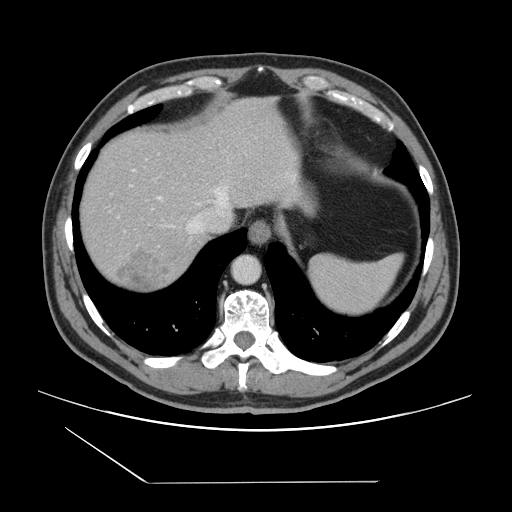
Contrast-enhanced abdominal CT, one axial slice. Position 124 of 157 along the scan axis. 120 kVp. Intravenous contrast given. Soft-tissue window (W 400 / L 40 HU). 512 × 512 image matrix, field of view 407 × 407 mm. Male patient, age 61 years. From the clinical record (not read from this slice): diagnosis: colorectal cancer liver metastases, imaged before liver resection; multiple liver metastases: yes.
Outlined on this slice (manually delineated by an expert):
- hepatic veins: bounding box (x1, y1, x2, y2) in pixels: (158, 187, 230, 234)
- liver: (79, 98, 294, 294)
- planned liver remnant (the part of the liver to remain after resection): (80, 107, 233, 230)
- liver metastasis: (113, 248, 174, 293)